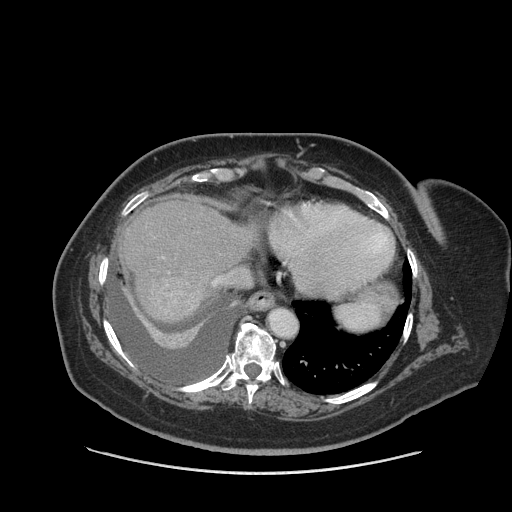
Contrast-enhanced abdominal CT (liver protocol), one axial slice. Slice 74 of 91 in the series (ordered by position). 140 kVp. Soft-tissue window (W 400 / L 40 HU). 512 × 512 image matrix. Case-level facts recorded for this patient, not image findings: diagnosis: hepatocellular carcinoma (patient treated with transarterial chemoembolisation; whether this scan precedes or follows treatment is not stated here); TNM stage (as recorded): Stage-I; Child-Pugh class: A; tumour differentiation: well differentiated; tumour nodularity: uninodular.
Outlined on this slice (semi-automatically segmented with operator editing):
- abdominal aorta: bounding box (x1, y1, x2, y2) in pixels: (269, 309, 297, 338)
- liver parenchyma outside the tumour (the mass and vessels are separate outlines, so this box may not span the whole liver): (118, 196, 256, 322)